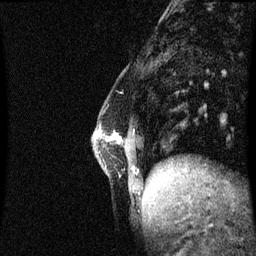
Breast MRI (dynamic contrast-enhanced), one sagittal slice; slice 18 of 60 in the series (ordered by position); dynamic contrast-enhanced series, image 2 of 3 at this slice position (ordered by acquisition); 1.5 T; TE 4.2 ms, TR 8.9 ms; 2.2 mm slice thickness; 256 × 256 image matrix, field of view 210 × 210 mm. Female patient, age 47 years. Case-level facts recorded for this patient, not image findings: setting: breast cancer imaged before/during neoadjuvant chemotherapy; receptor status: HR-positive, HER2-negative.
Annotated regions visible in this slice (semi-automatic segmentation, software-assisted and operator-edited):
- analysis volume of interest (the breast-tissue region the enhancement analysis was run in; not a lesion): bounding box <93,130,139,192> (left, top, right, bottom; pixels)
- tumour enhancement mask (voxels above the 70 % enhancement threshold inside the analysis volume of interest): <114,135,120,141>